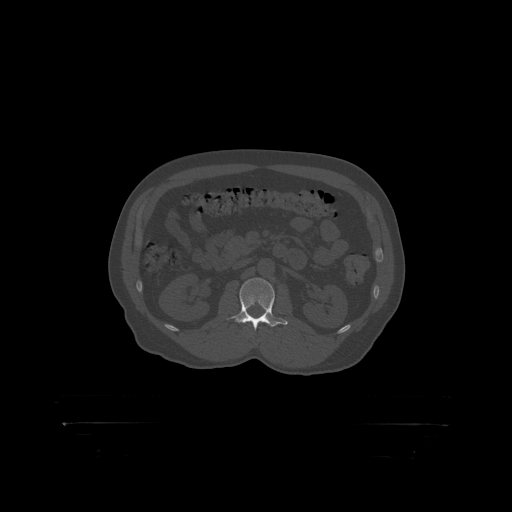
CT including the spine, one axial slice; position 298 of 399 along the scan axis; 120 kVp; bone window (W 1800 / L 400 HU); 512 × 512 image matrix. Patient: male, 46 years. Case-level facts recorded for this patient, not image findings: primary cancer: skin.
Outlined on this slice (semi-automatic segmentation, software-assisted and operator-edited):
- L2 vertebra: bounding box (x1, y1, x2, y2) in pixels: (237, 278, 275, 319)